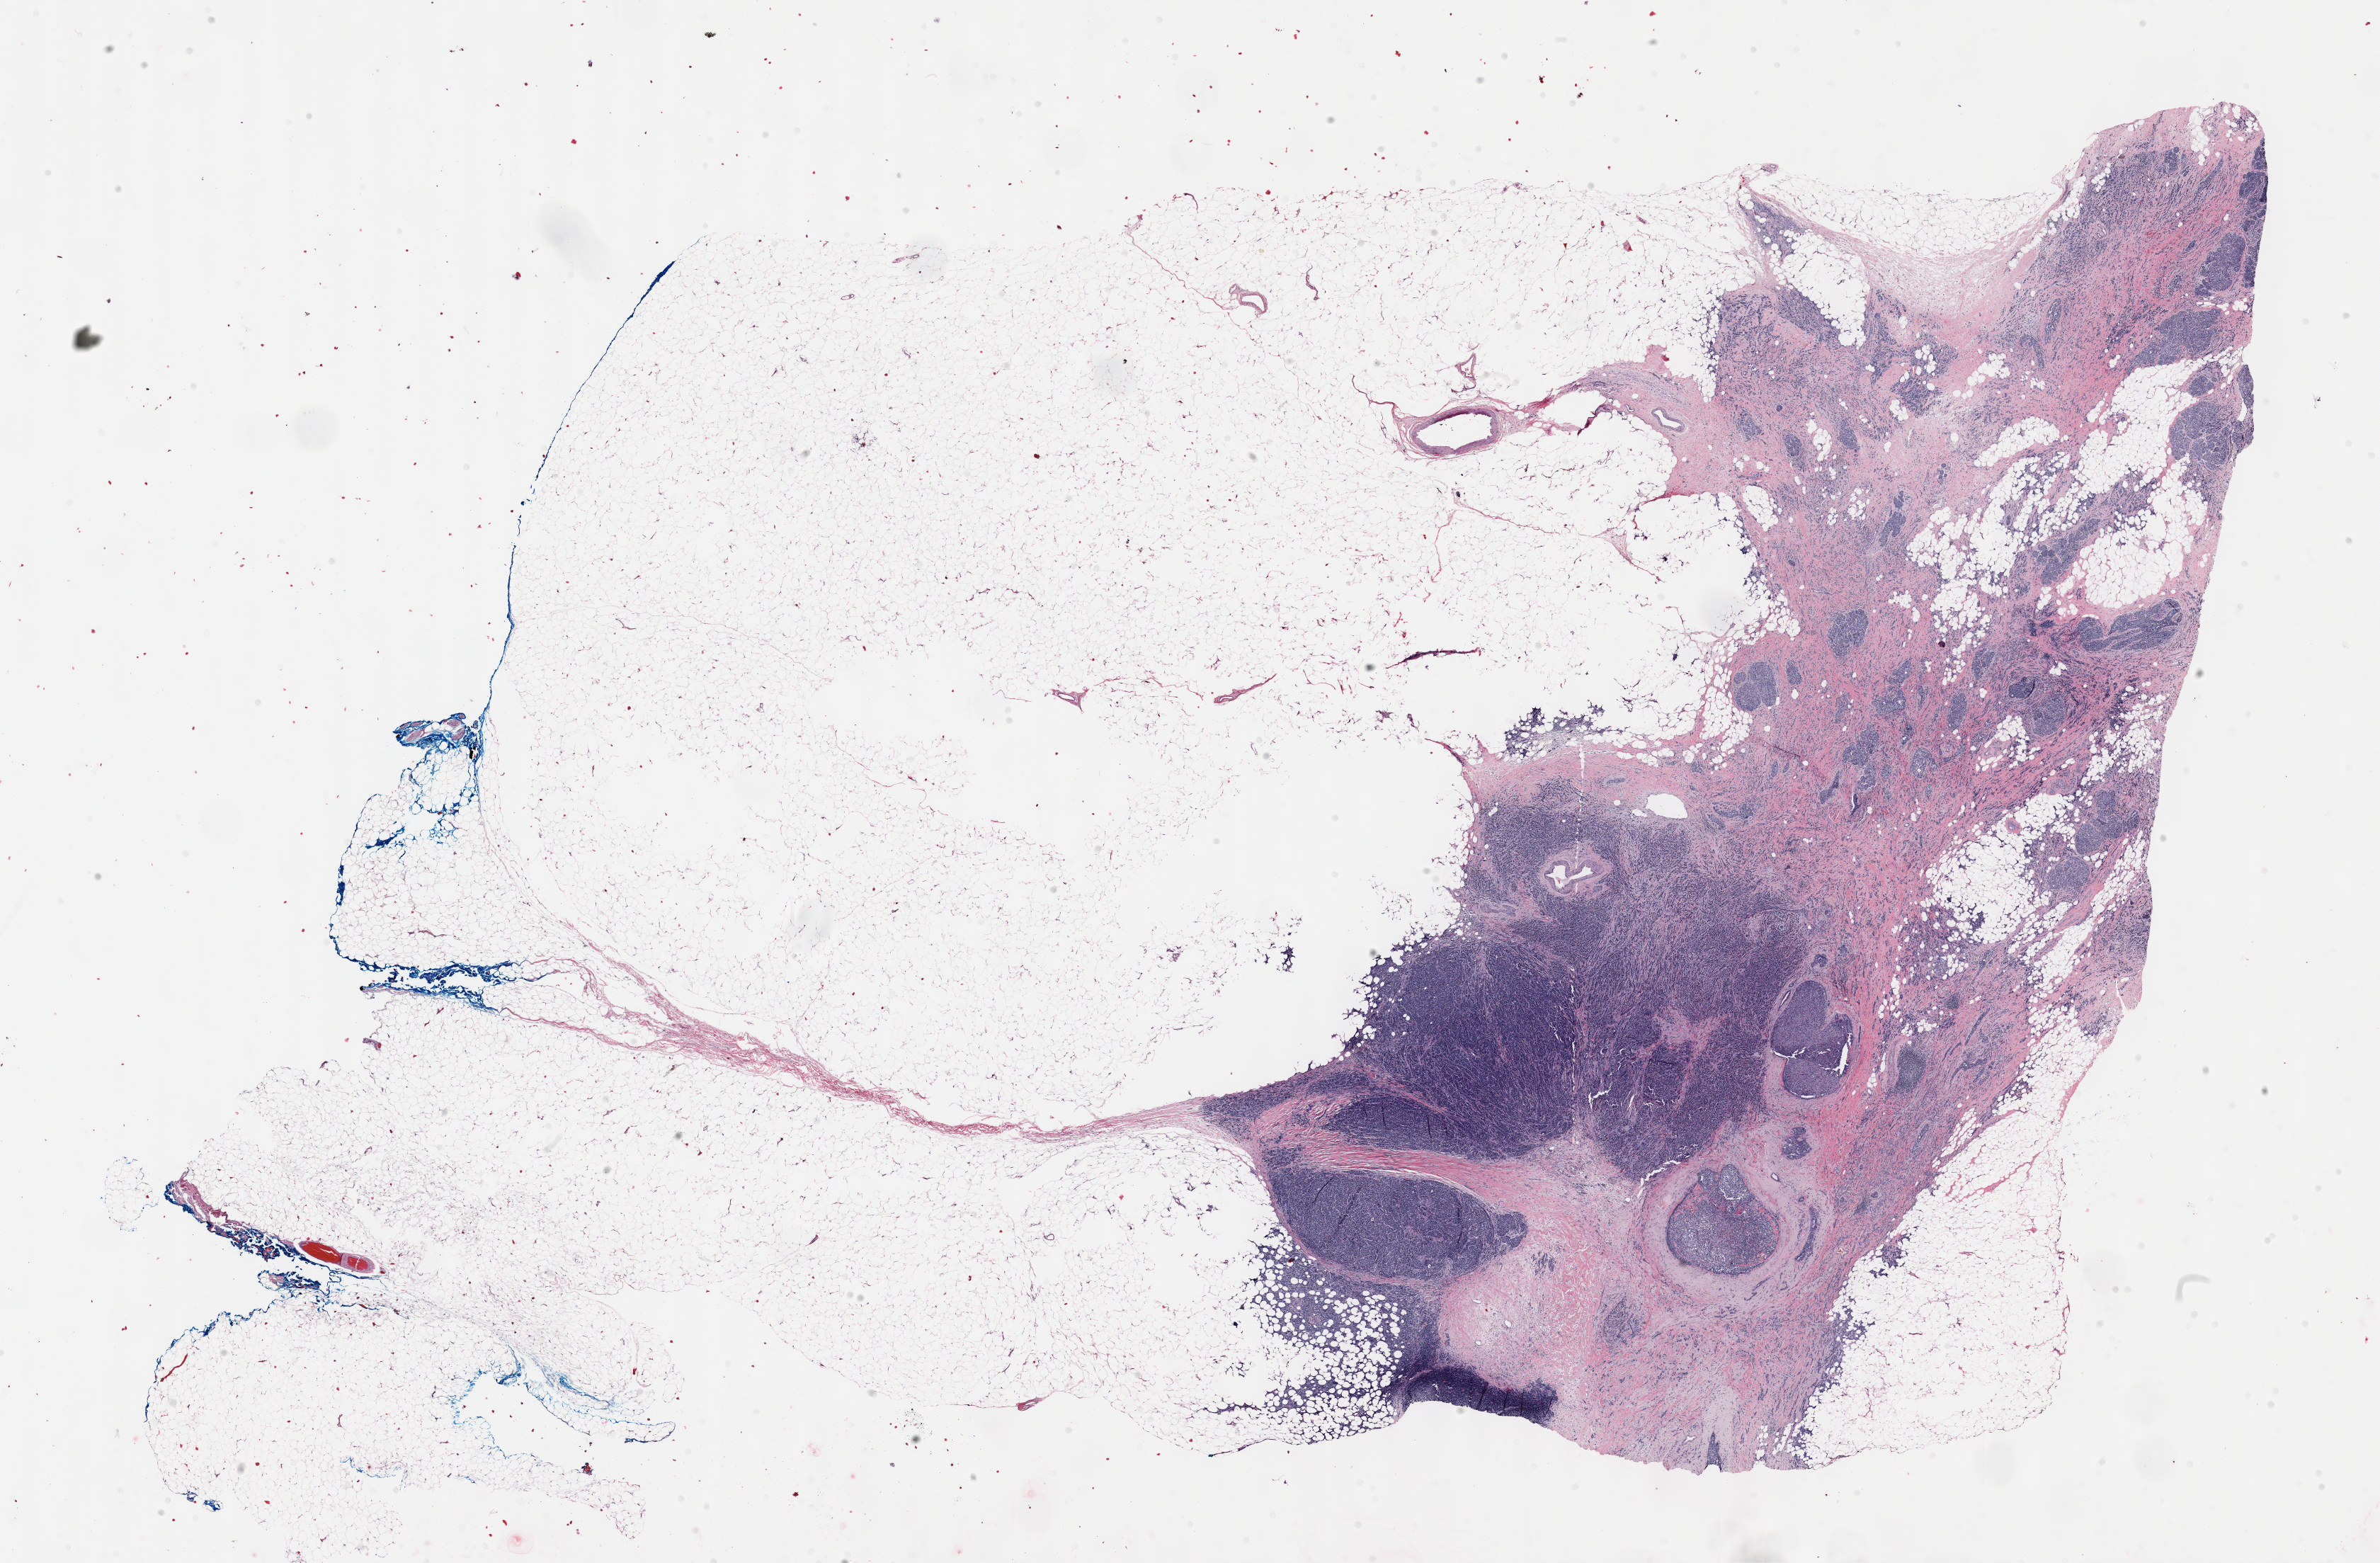
H&E whole-slide image, a low-resolution overview of the entire scanned area, about 27.2 x 17.8 mm. FFPE section. Breast, primary tumour sample. Female patient; age at initial diagnosis 54 years.
Pathologic diagnosis: Infiltrating lobular mixed with other types of carcinoma (upper-inner quadrant of breast). Lymph nodes positive (case pathology): 2 of 18 examined. AJCC pathologic stage: IIB (7th edition). Laterality: right.